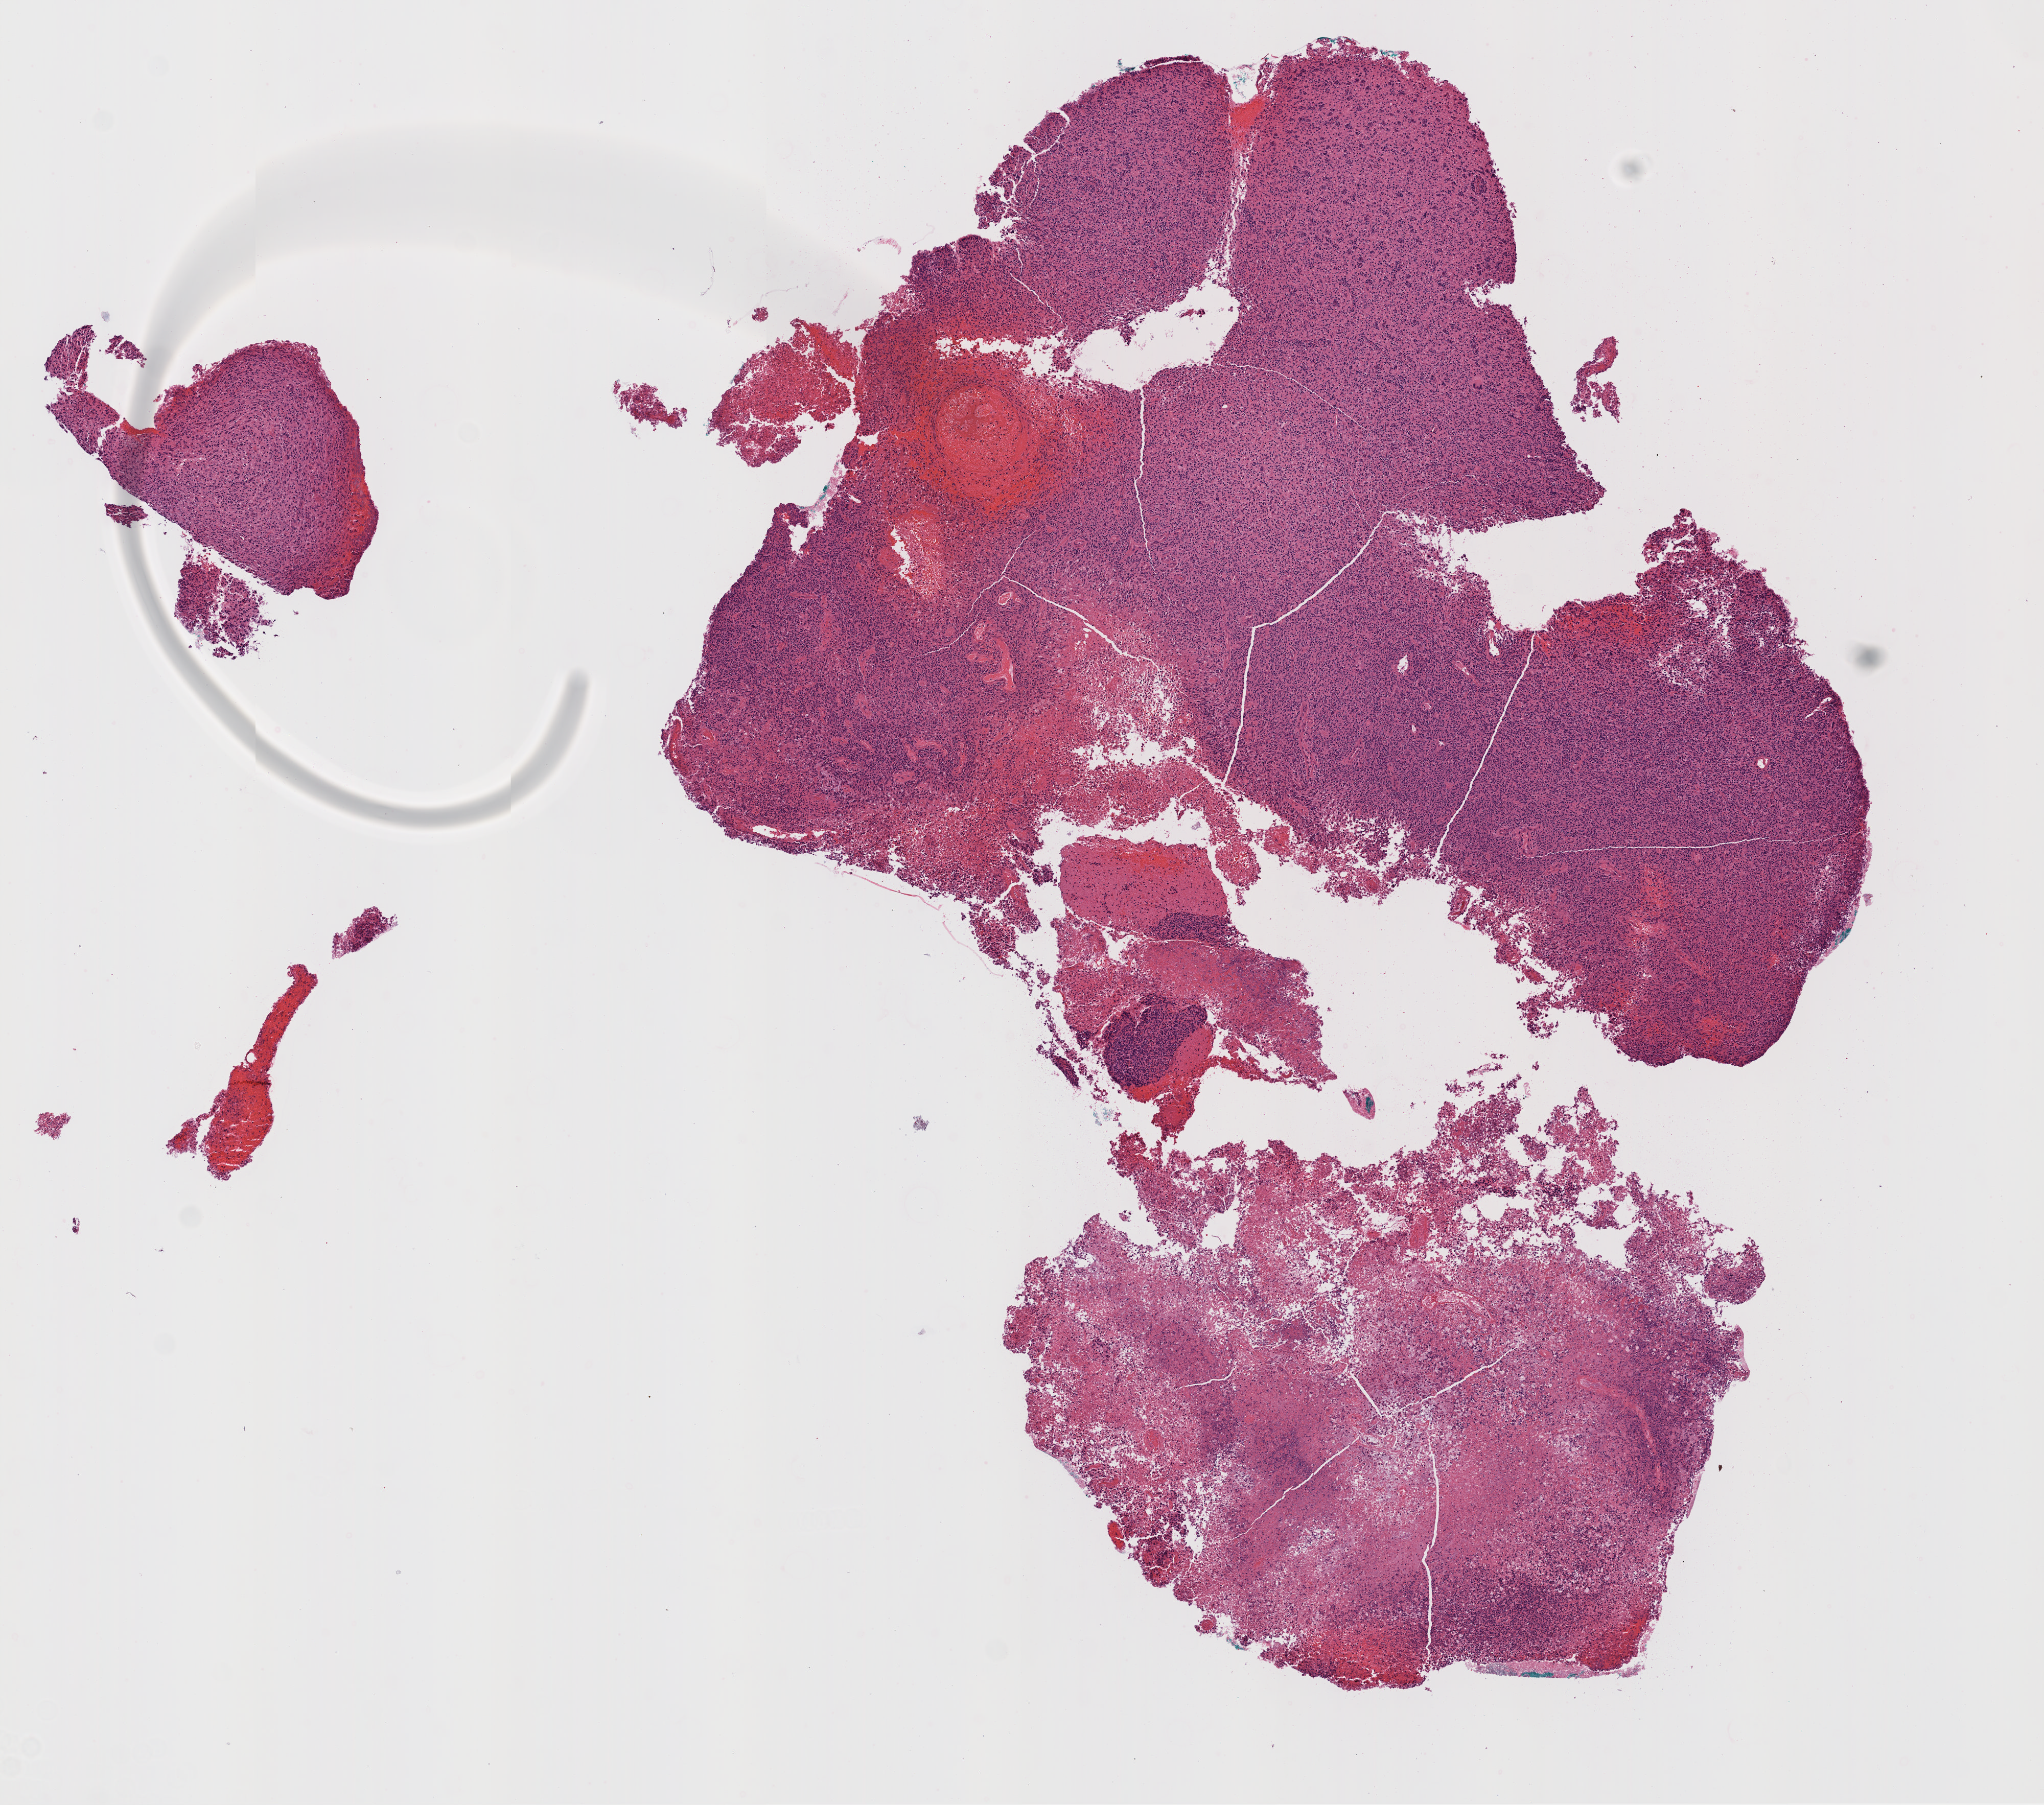
H&E-stained whole-slide image, shown as a low-resolution overview of the whole scanned area (about 8.0 x 7.1 mm). Formalin-fixed paraffin-embedded (FFPE) diagnostic section. Sample: primary tumour, brain. Patient: female, age at initial diagnosis 59 years.
Diagnosis: Glioblastoma.